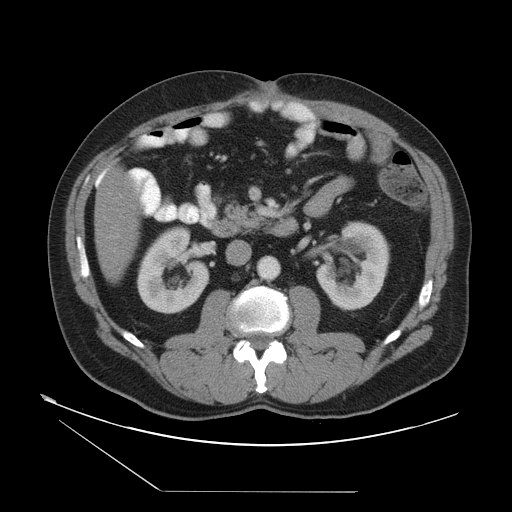
Contrast-enhanced abdominal CT, one axial slice. Position 16 of 55 along the scan axis. Reconstruction kernel STANDARD. 120 kVp. Soft-tissue window (W 400 / L 40 HU). 512 × 512 image matrix, field of view 454 × 454 mm. Male patient, age 59 years. Case-level facts recorded for this patient, not image findings: diagnosis: colorectal cancer liver metastases, imaged before liver resection; multiple liver metastases: yes; largest metastasis: 0.3 cm; disease in both lobes: yes.
Structures marked on this image (expert manual segmentation):
- hepatic veins: box from (x=107, y=170) to (x=135, y=209) px
- liver: (x=95, y=167)–(x=142, y=279)
- planned liver remnant (the part of the liver to remain after resection): (x=95, y=167)–(x=142, y=280)